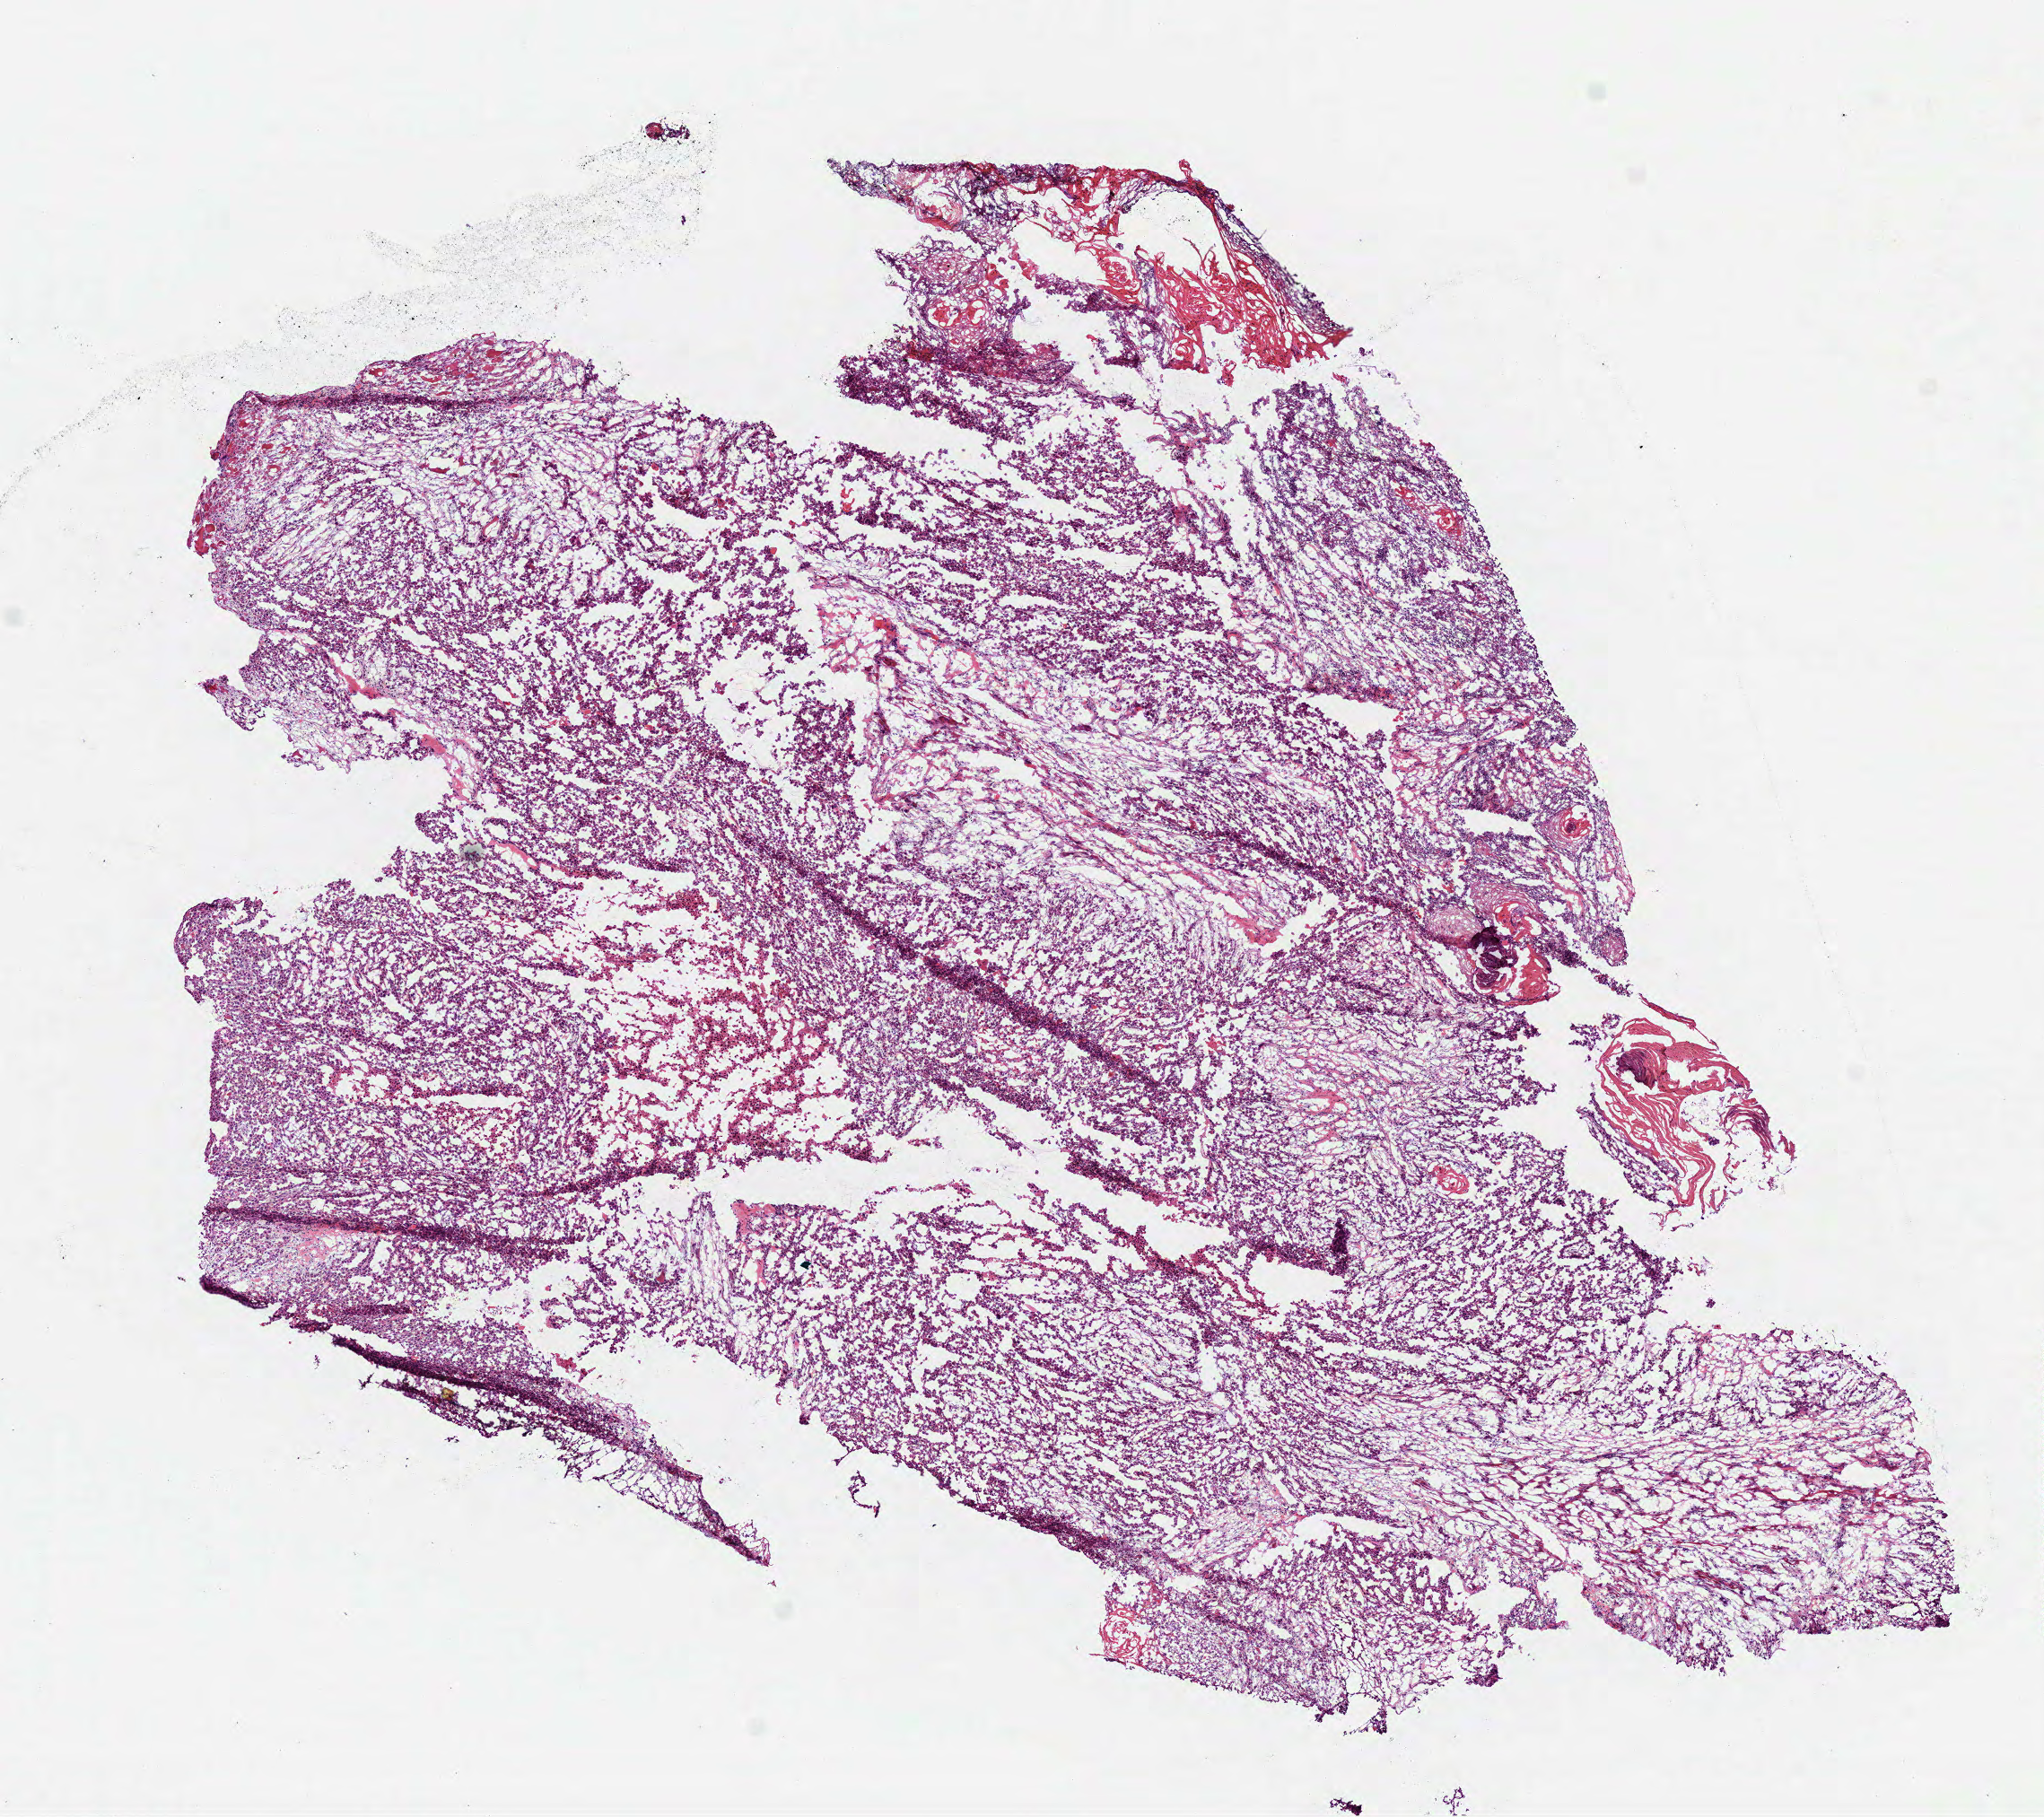
Whole-slide histology image, H&E-stained — low-resolution overview of the scanned area, about 9.2 x 8.2 mm. Frozen section from the top of the tissue portion. Head and neck, primary tumour sample. Female, age 48 years at initial diagnosis. Histologic grade: GX (grade cannot be assessed). Composition of this section per pathologist review: tumour cells 73%, tumour nuclei 70%, normal cells 0%, stromal cells 15%, necrosis 12%.
Diagnosis: Squamous cell carcinoma, NOS (overlapping lesion of lip, oral cavity and pharynx). AJCC pathologic stage: IVA (7th edition).